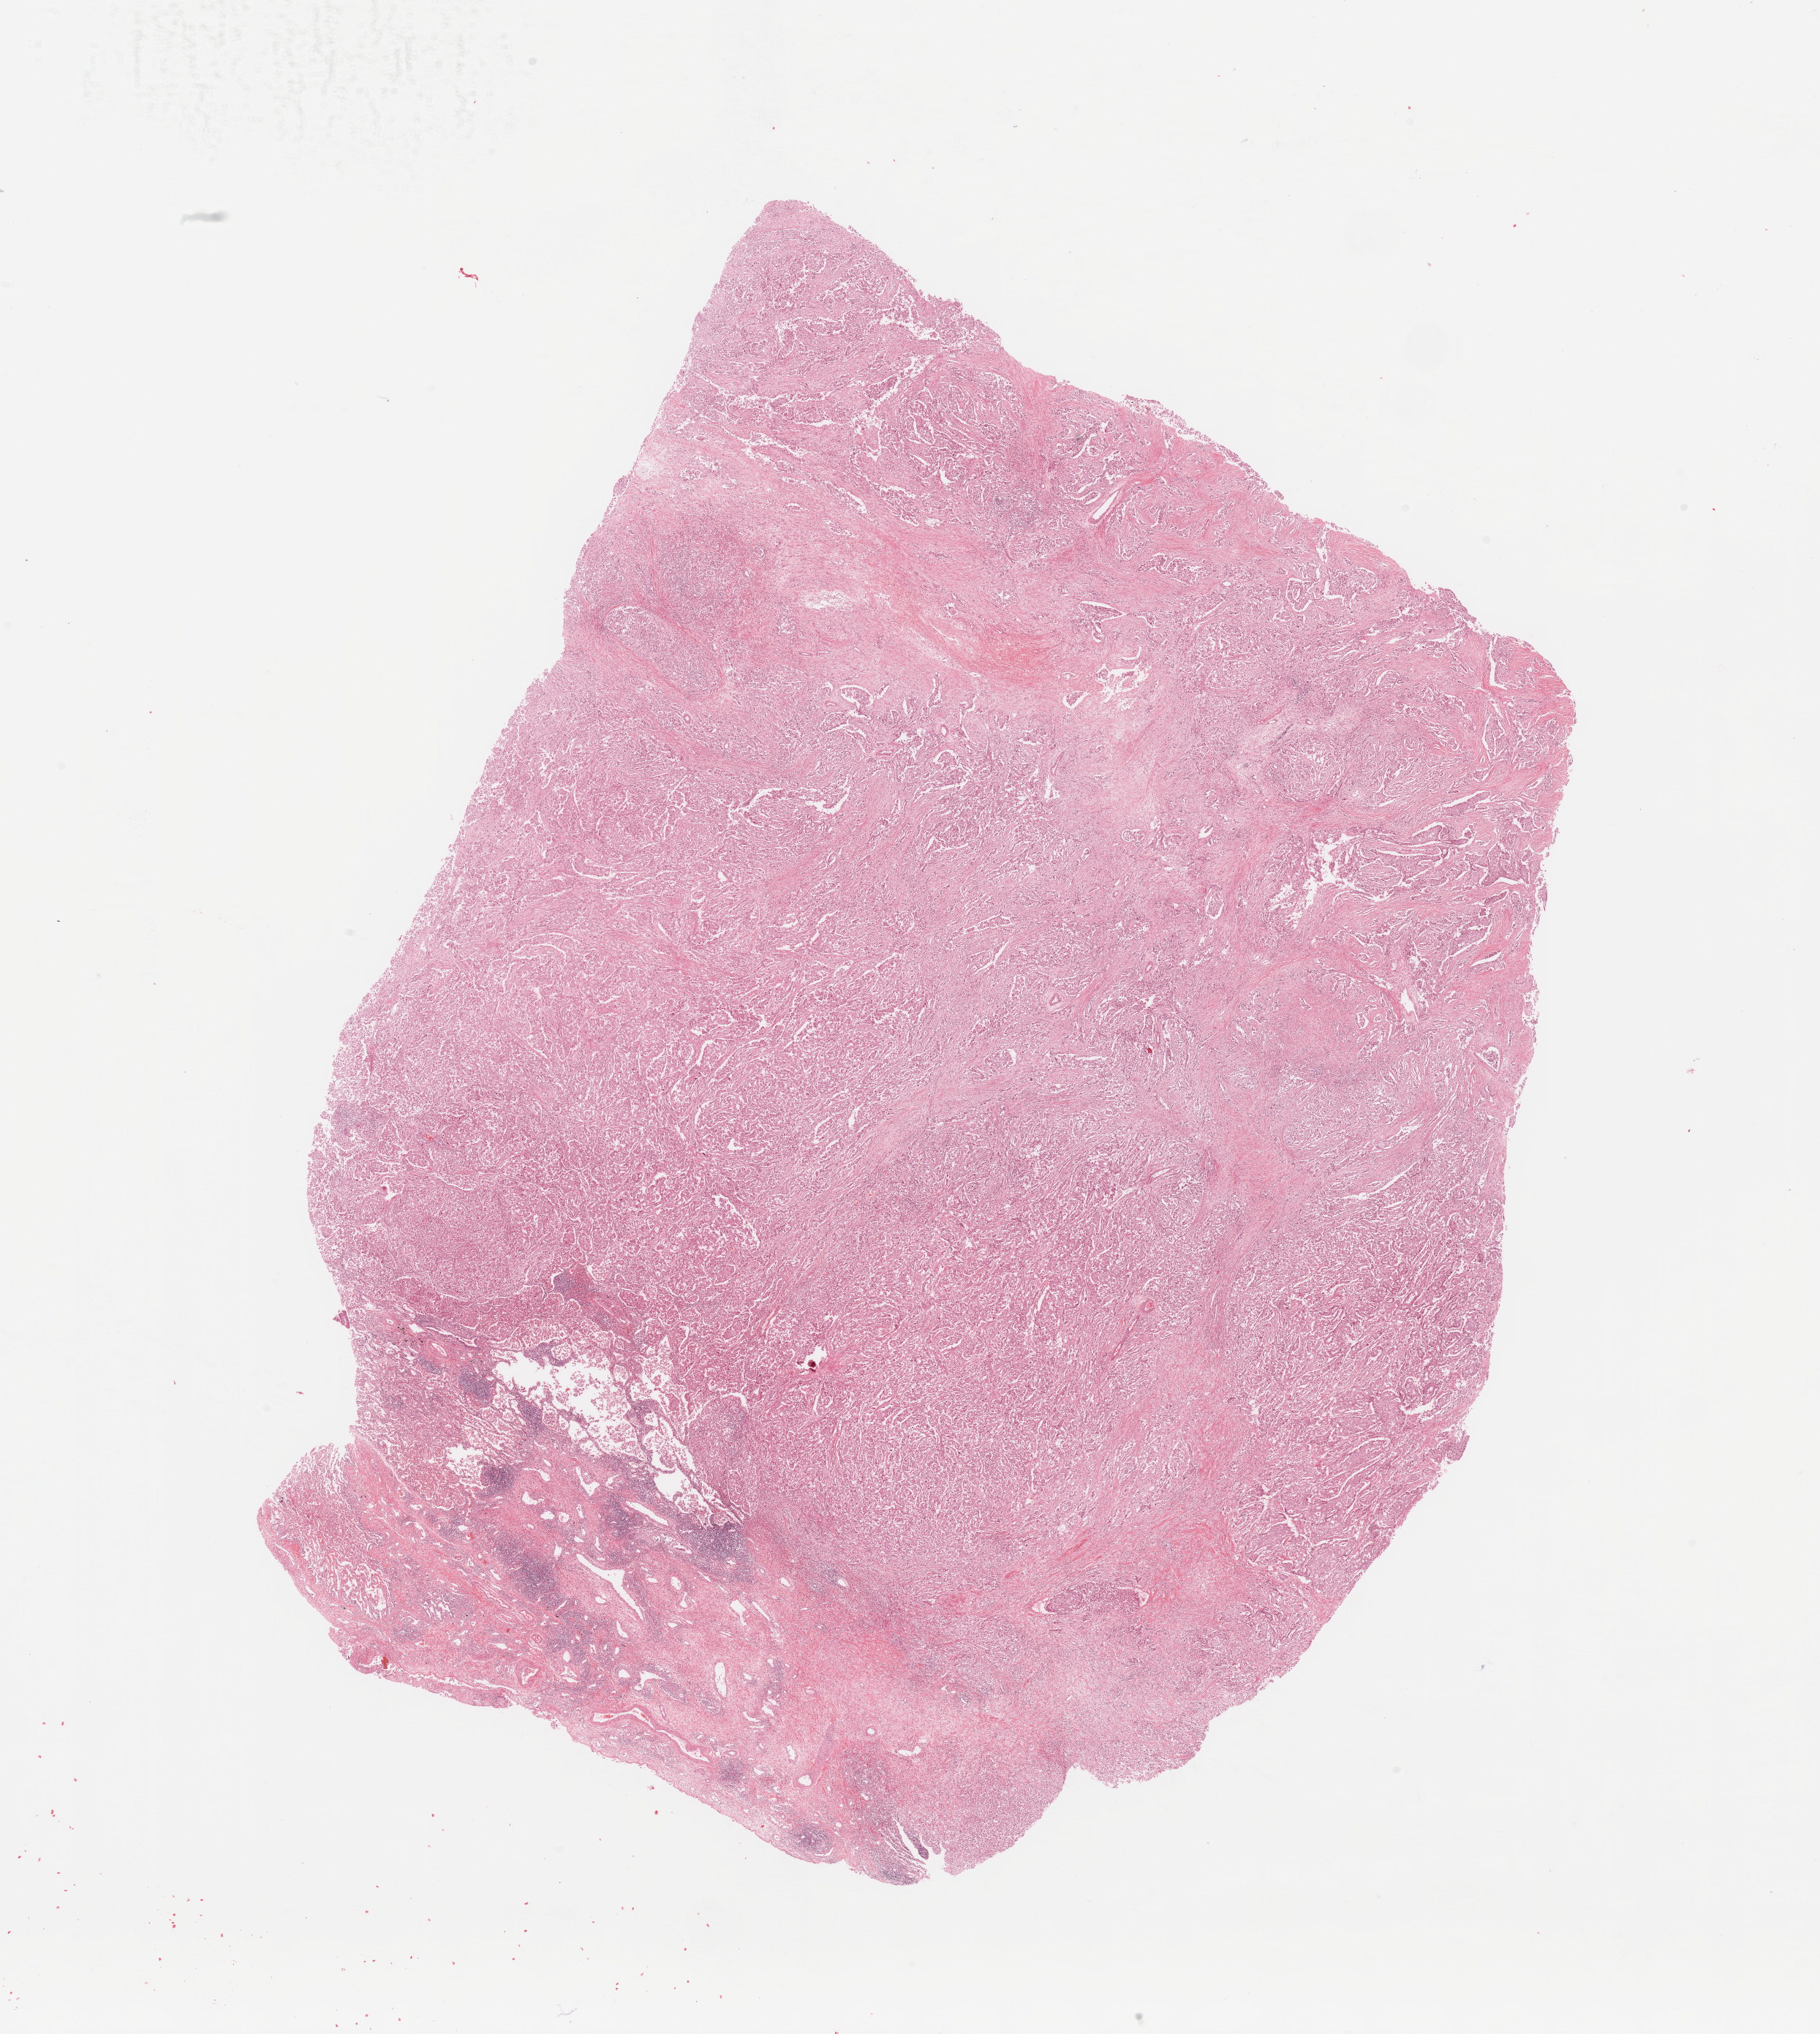
Whole-slide histology image, H&E-stained, whole scanned area (about 19.7 x 22.0 mm) shown as a low-resolution overview; tumour tissue sample, lung. Female, 49 y/o. Histologic grade: G3 (poorly differentiated).
* diagnosis: Adenocarcinoma, NOS
* AJCC pathologic stage: IB